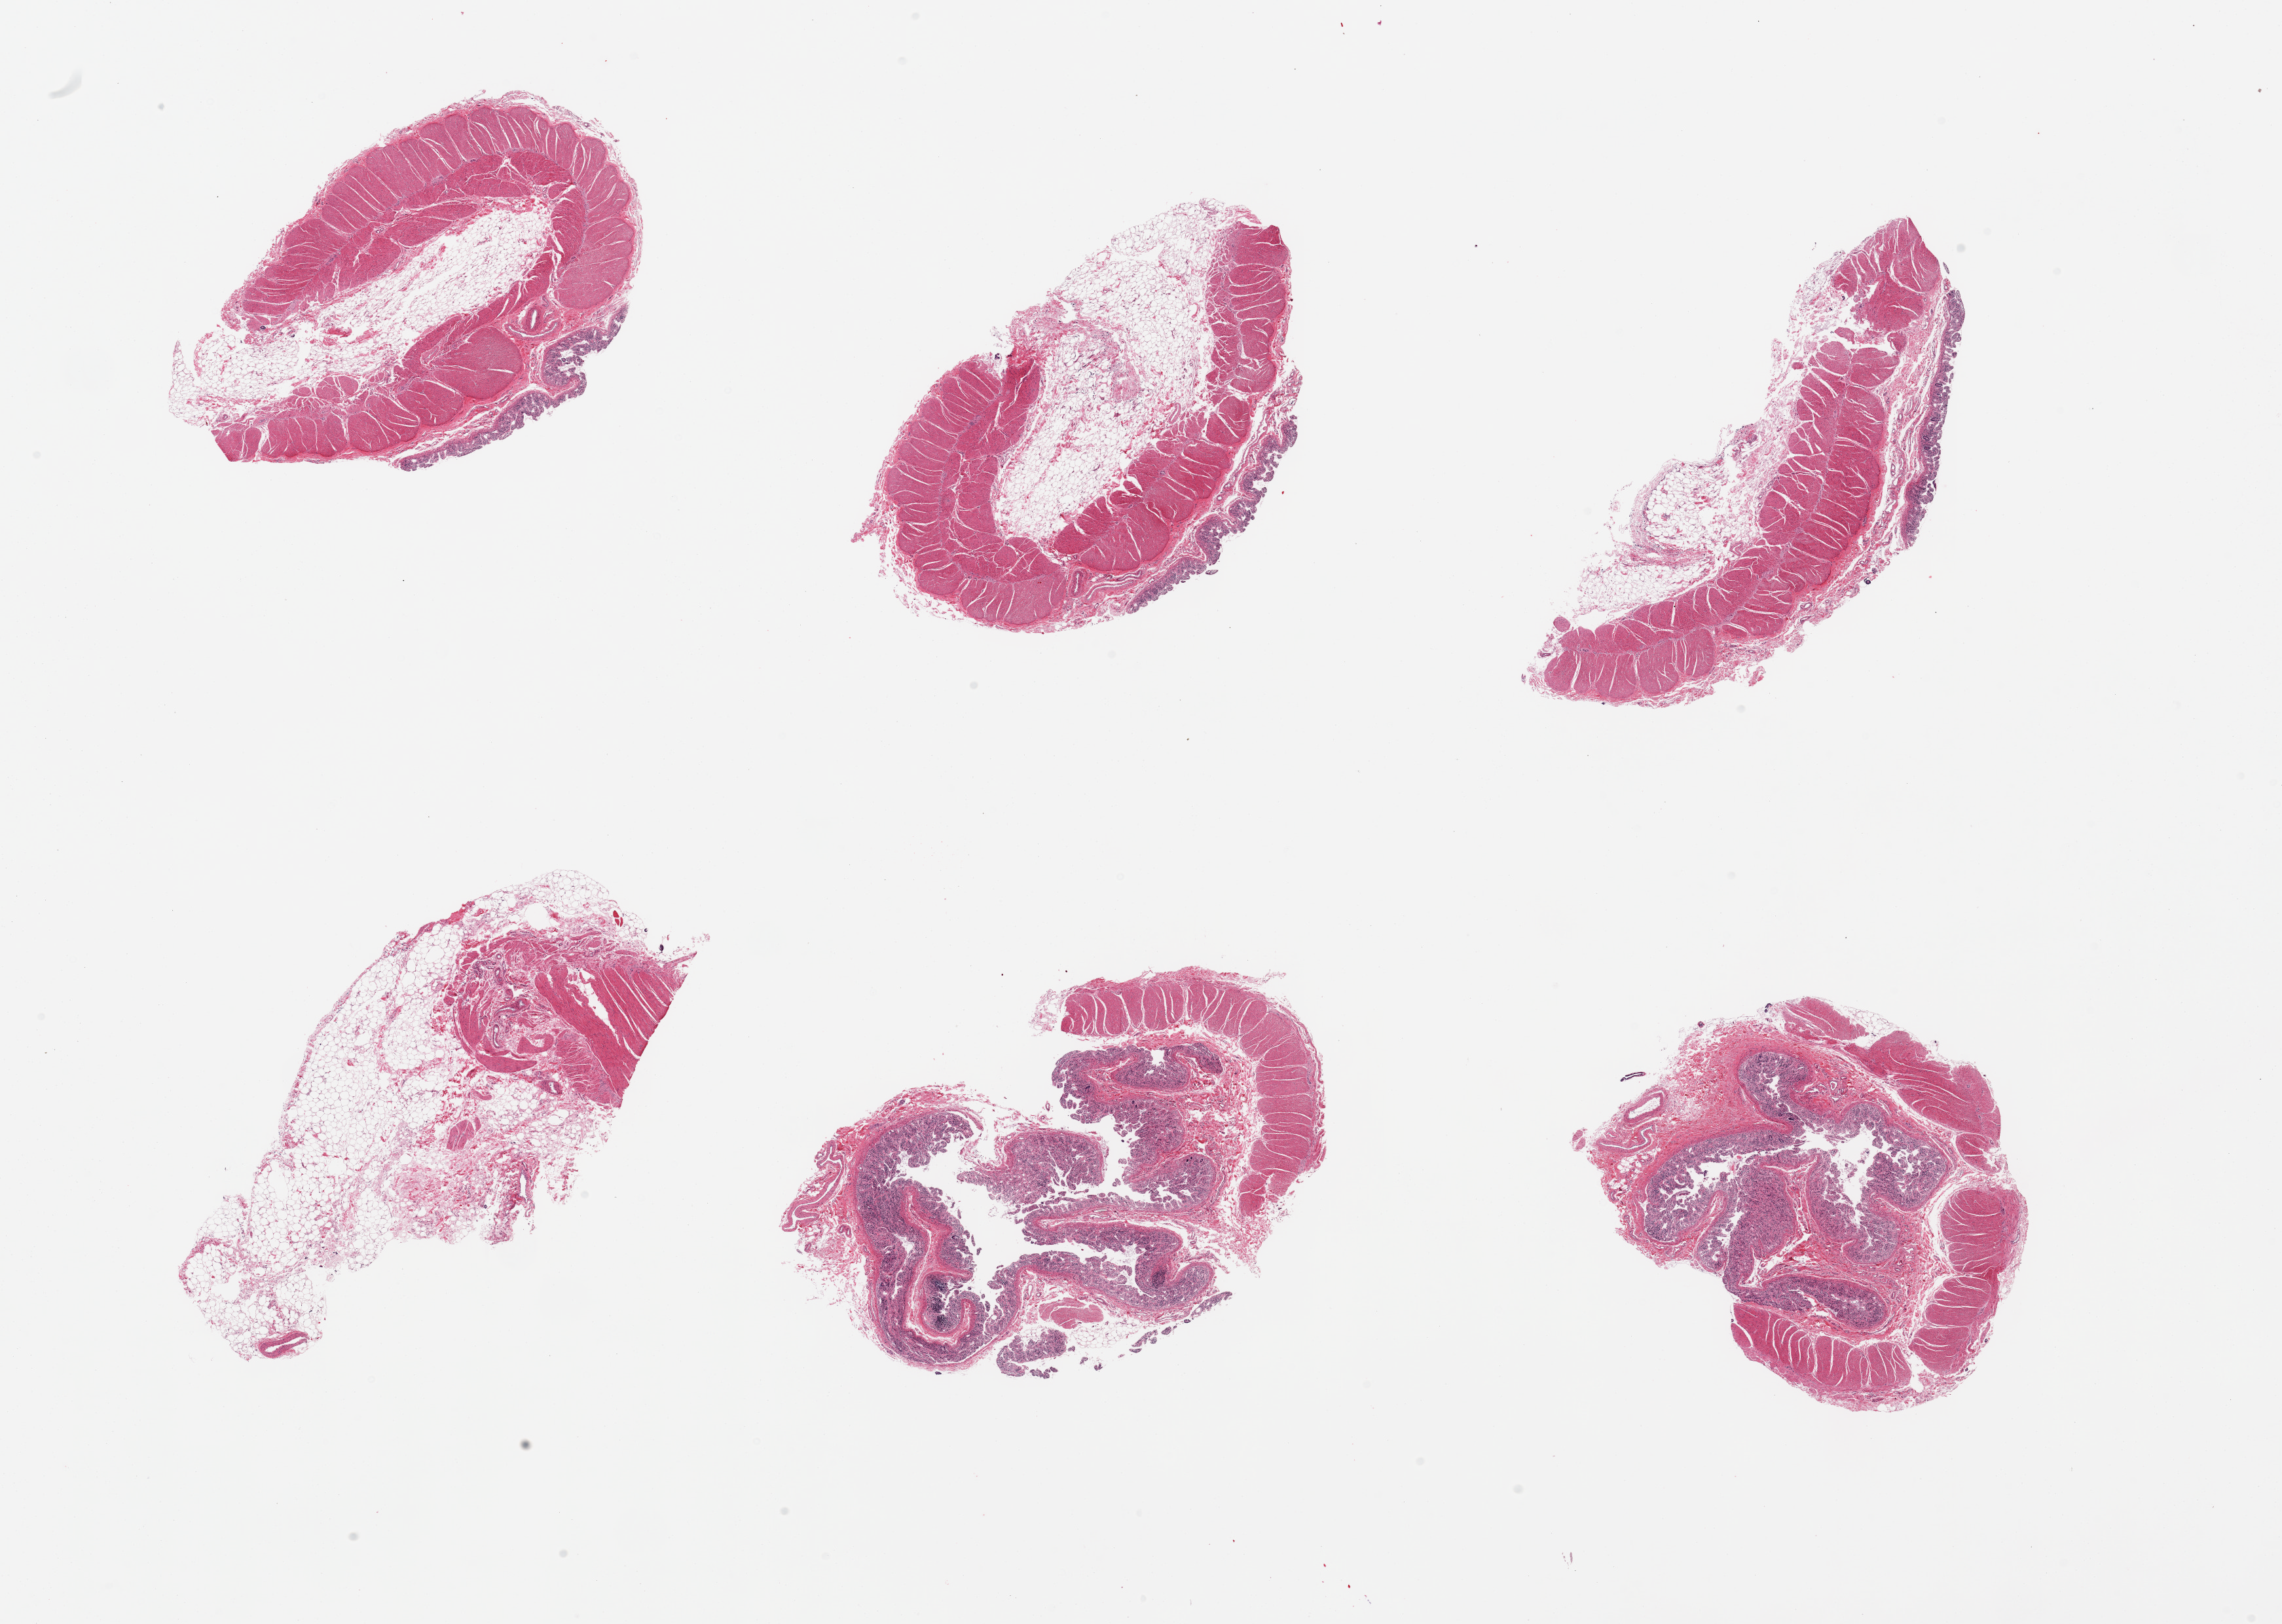
Hematoxylin and eosin (H&E) whole-slide image — shown as a low-resolution overview of the whole scanned area (about 27.6 x 19.6 mm). PAXgene-fixed, paraffin-embedded tissue. Target tissue: ileum. Tissue donor sample. Donor sex: female.
* reviewer comment on this tissue sample: 6 pieces; all with muscularis and no lymphoid content in autolyzed mucosa